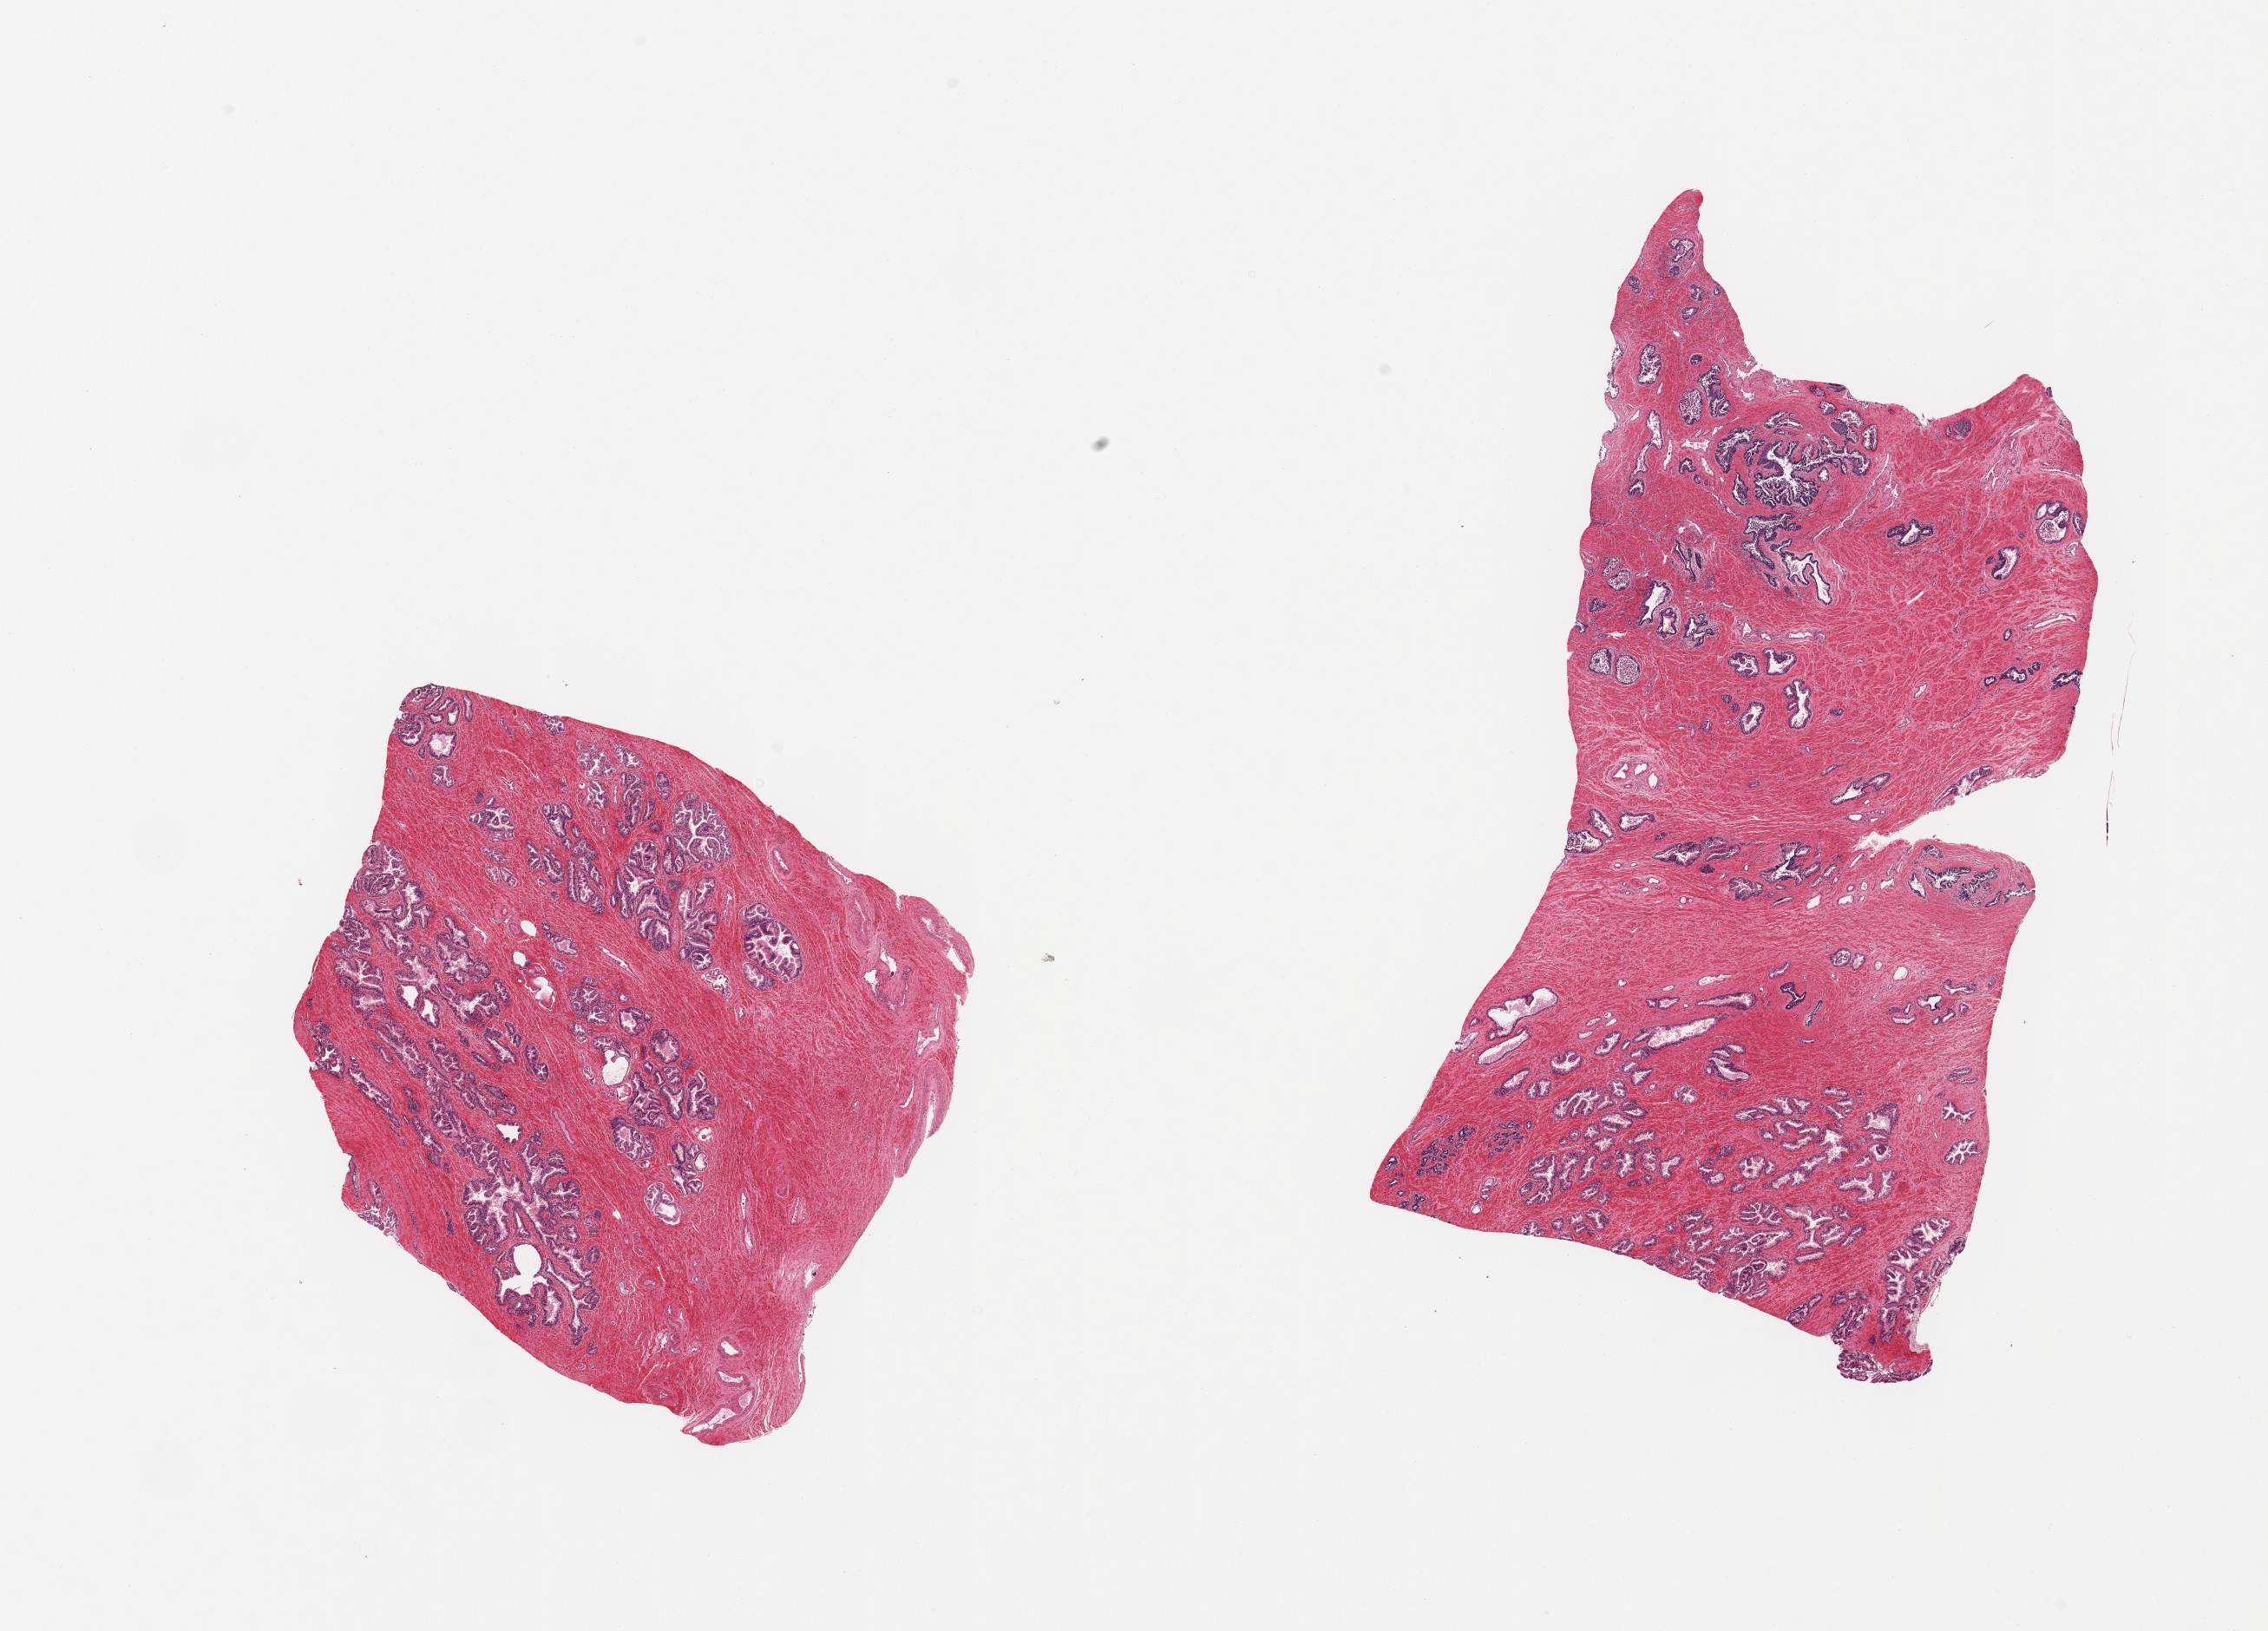
Digitized haematoxylin and eosin-stained section — whole scanned area (about 20.7 x 14.9 mm) shown as a low-resolution overview; PAXgene-fixed, paraffin-embedded tissue; sampled site (target tissue): prostate; donor tissue sample. Donor sex: male.
Reviewer comment on this tissue sample: 2 pieces, hyperplastic glandular pattern.